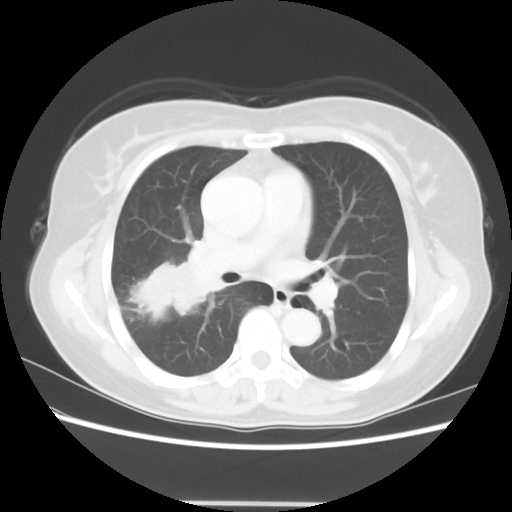
Chest CT, one axial slice; position 34 of 56 along the scan axis; reconstruction kernel STANDARD; 120 kVp; lung window (W 1500 / L -600 HU); 5 mm slice thickness; 512 × 512 image matrix. Female patient, age 55 years. From the clinical record (not read from this slice): clinical TNM (as recorded): T2 N1 M0.
Annotated regions visible in this slice (rectangle marked by the reading radiologist):
- lung tumour (recorded histology: adenocarcinoma): box from (x=126, y=256) to (x=225, y=331) px